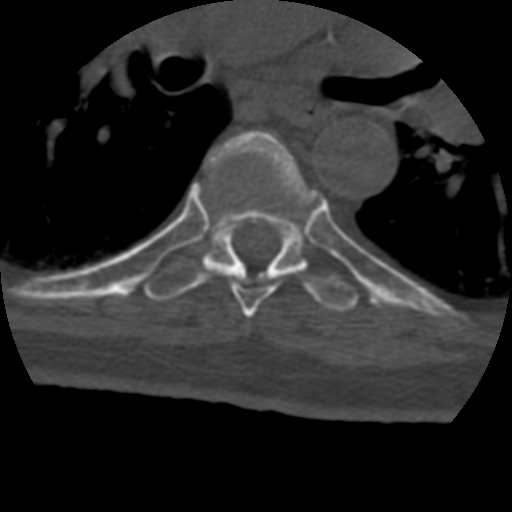
CT including the spine, one axial slice. Slice 291 of 399 in the series (ordered by position). Reconstruction kernel STANDARD. 120 kVp. Bone window (W 1800 / L 400 HU). 1.25 mm slice thickness. 512 × 512 image matrix. Patient age 69 years. From the clinical record (not read from this slice): primary cancer: prostate.
Outlined on this slice (semi-automatically segmented with operator editing):
- T6 vertebra: bounding box (x1, y1, x2, y2) in pixels: (206, 131, 313, 317)
- T7 vertebra: (144, 153, 359, 311)